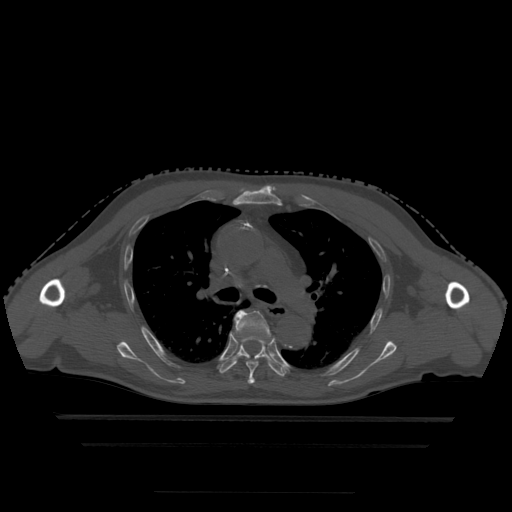
CT including the spine, one axial slice; slice 328 of 522 in the series (ordered by position); bone window (W 1800 / L 400 HU); 1.25 mm slice thickness; 512 × 512 image matrix. Patient age 68 years. From the clinical record (not read from this slice): primary cancer: urothelial.
Annotated regions visible in this slice (semi-automatic segmentation, software-assisted and operator-edited):
- T5 vertebra: bounding box (x1, y1, x2, y2) in pixels: (234, 310, 270, 384)
- T6 vertebra: (219, 337, 286, 377)